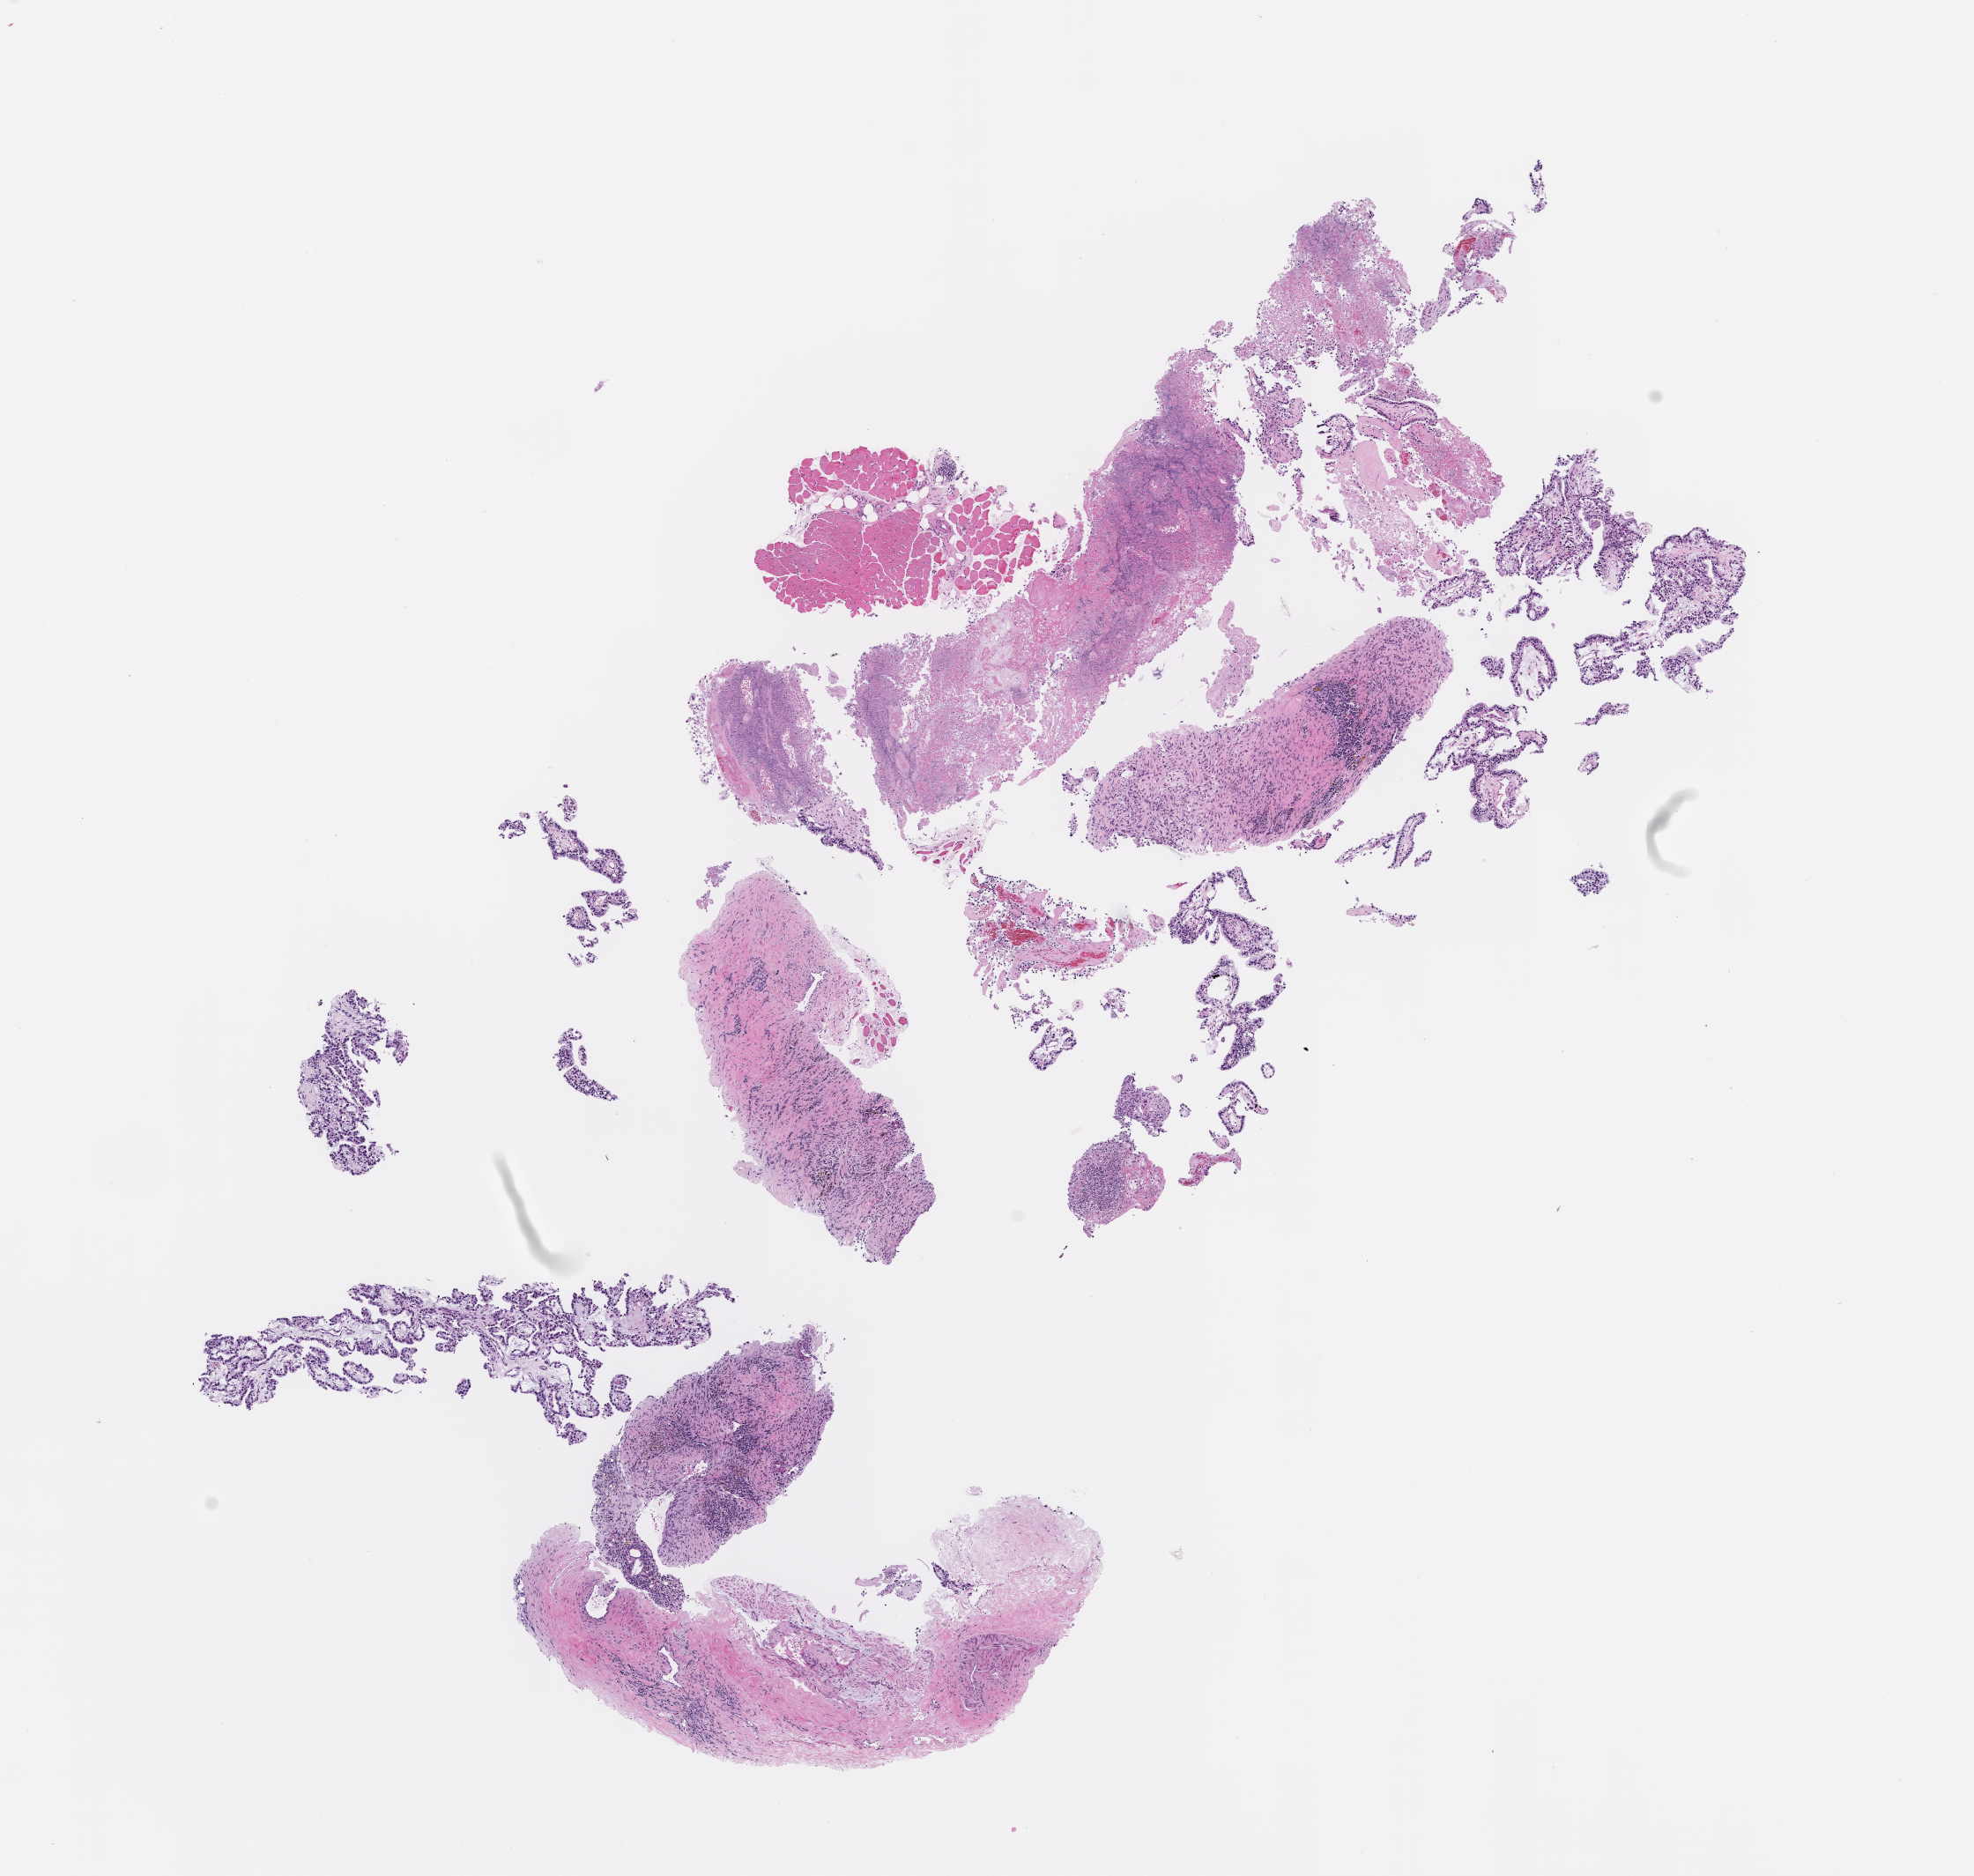
Digitized H&E-stained section — whole scanned area (about 9.0 x 8.6 mm) shown as a low-resolution overview, FFPE section. Patient sex: female.
• this section: metastatic tumor tissue
• patient diagnosis (primary): Ovarian Carcinoma